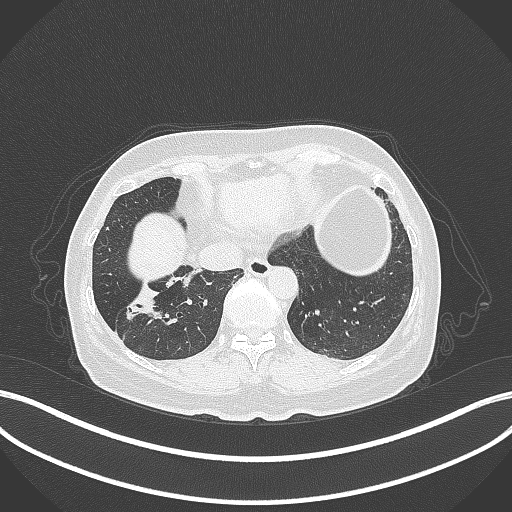
Chest CT, one axial slice. Position 102 of 429 along the scan axis. Reconstruction kernel B70f. Lung window (W 1500 / L -600 HU). 512 × 512 image matrix, field of view 400 × 400 mm. Patient: female, 67 years. From the clinical record (not read from this slice): clinical TNM (as recorded): T1c N1 M0; histopathological grade: G2-3.
Annotated regions visible in this slice (rectangle marked by the reading radiologist):
- lung tumour (recorded histology: adenocarcinoma): bounding box (x1, y1, x2, y2) in pixels: (123, 285, 174, 334)